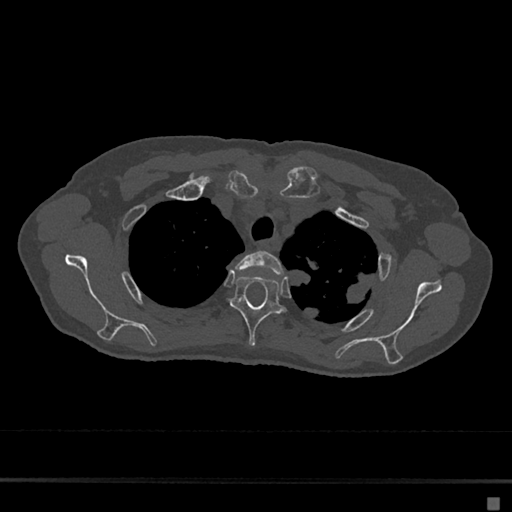
CT including the spine, one axial slice; slice 543 of 797 in the series (ordered by position); reconstruction kernel Br40s/3; 120 kVp; bone window (W 1800 / L 400 HU); 0.5 mm slice thickness; 512 × 512 image matrix. Patient: female, 68 years. From the clinical record (not read from this slice): primary cancer: renal.
Structures marked on this image (semi-automatic segmentation, software-assisted and operator-edited):
- T2 vertebra: bounding box [x1, y1, x2, y2] px = [236, 251, 284, 275]
- T3 vertebra: [230, 276, 285, 347]